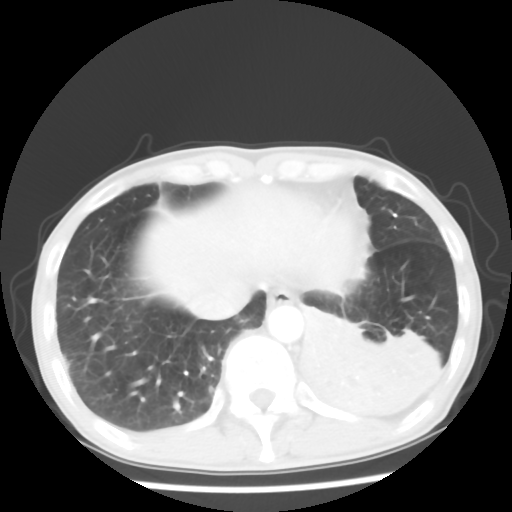
Chest CT, one axial slice. Slice 14 of 64 in the series (ordered by position). 120 kVp. Lung window (W 1500 / L -600 HU). 512 × 512 image matrix. Male patient, age 68 years. From the clinical record (not read from this slice): clinical TNM (as recorded): T4 N0 M0.
Annotated regions visible in this slice (bounding box drawn by a radiologist):
- lung tumour (recorded histology: squamous cell carcinoma): box from (x=292, y=303) to (x=439, y=442) px